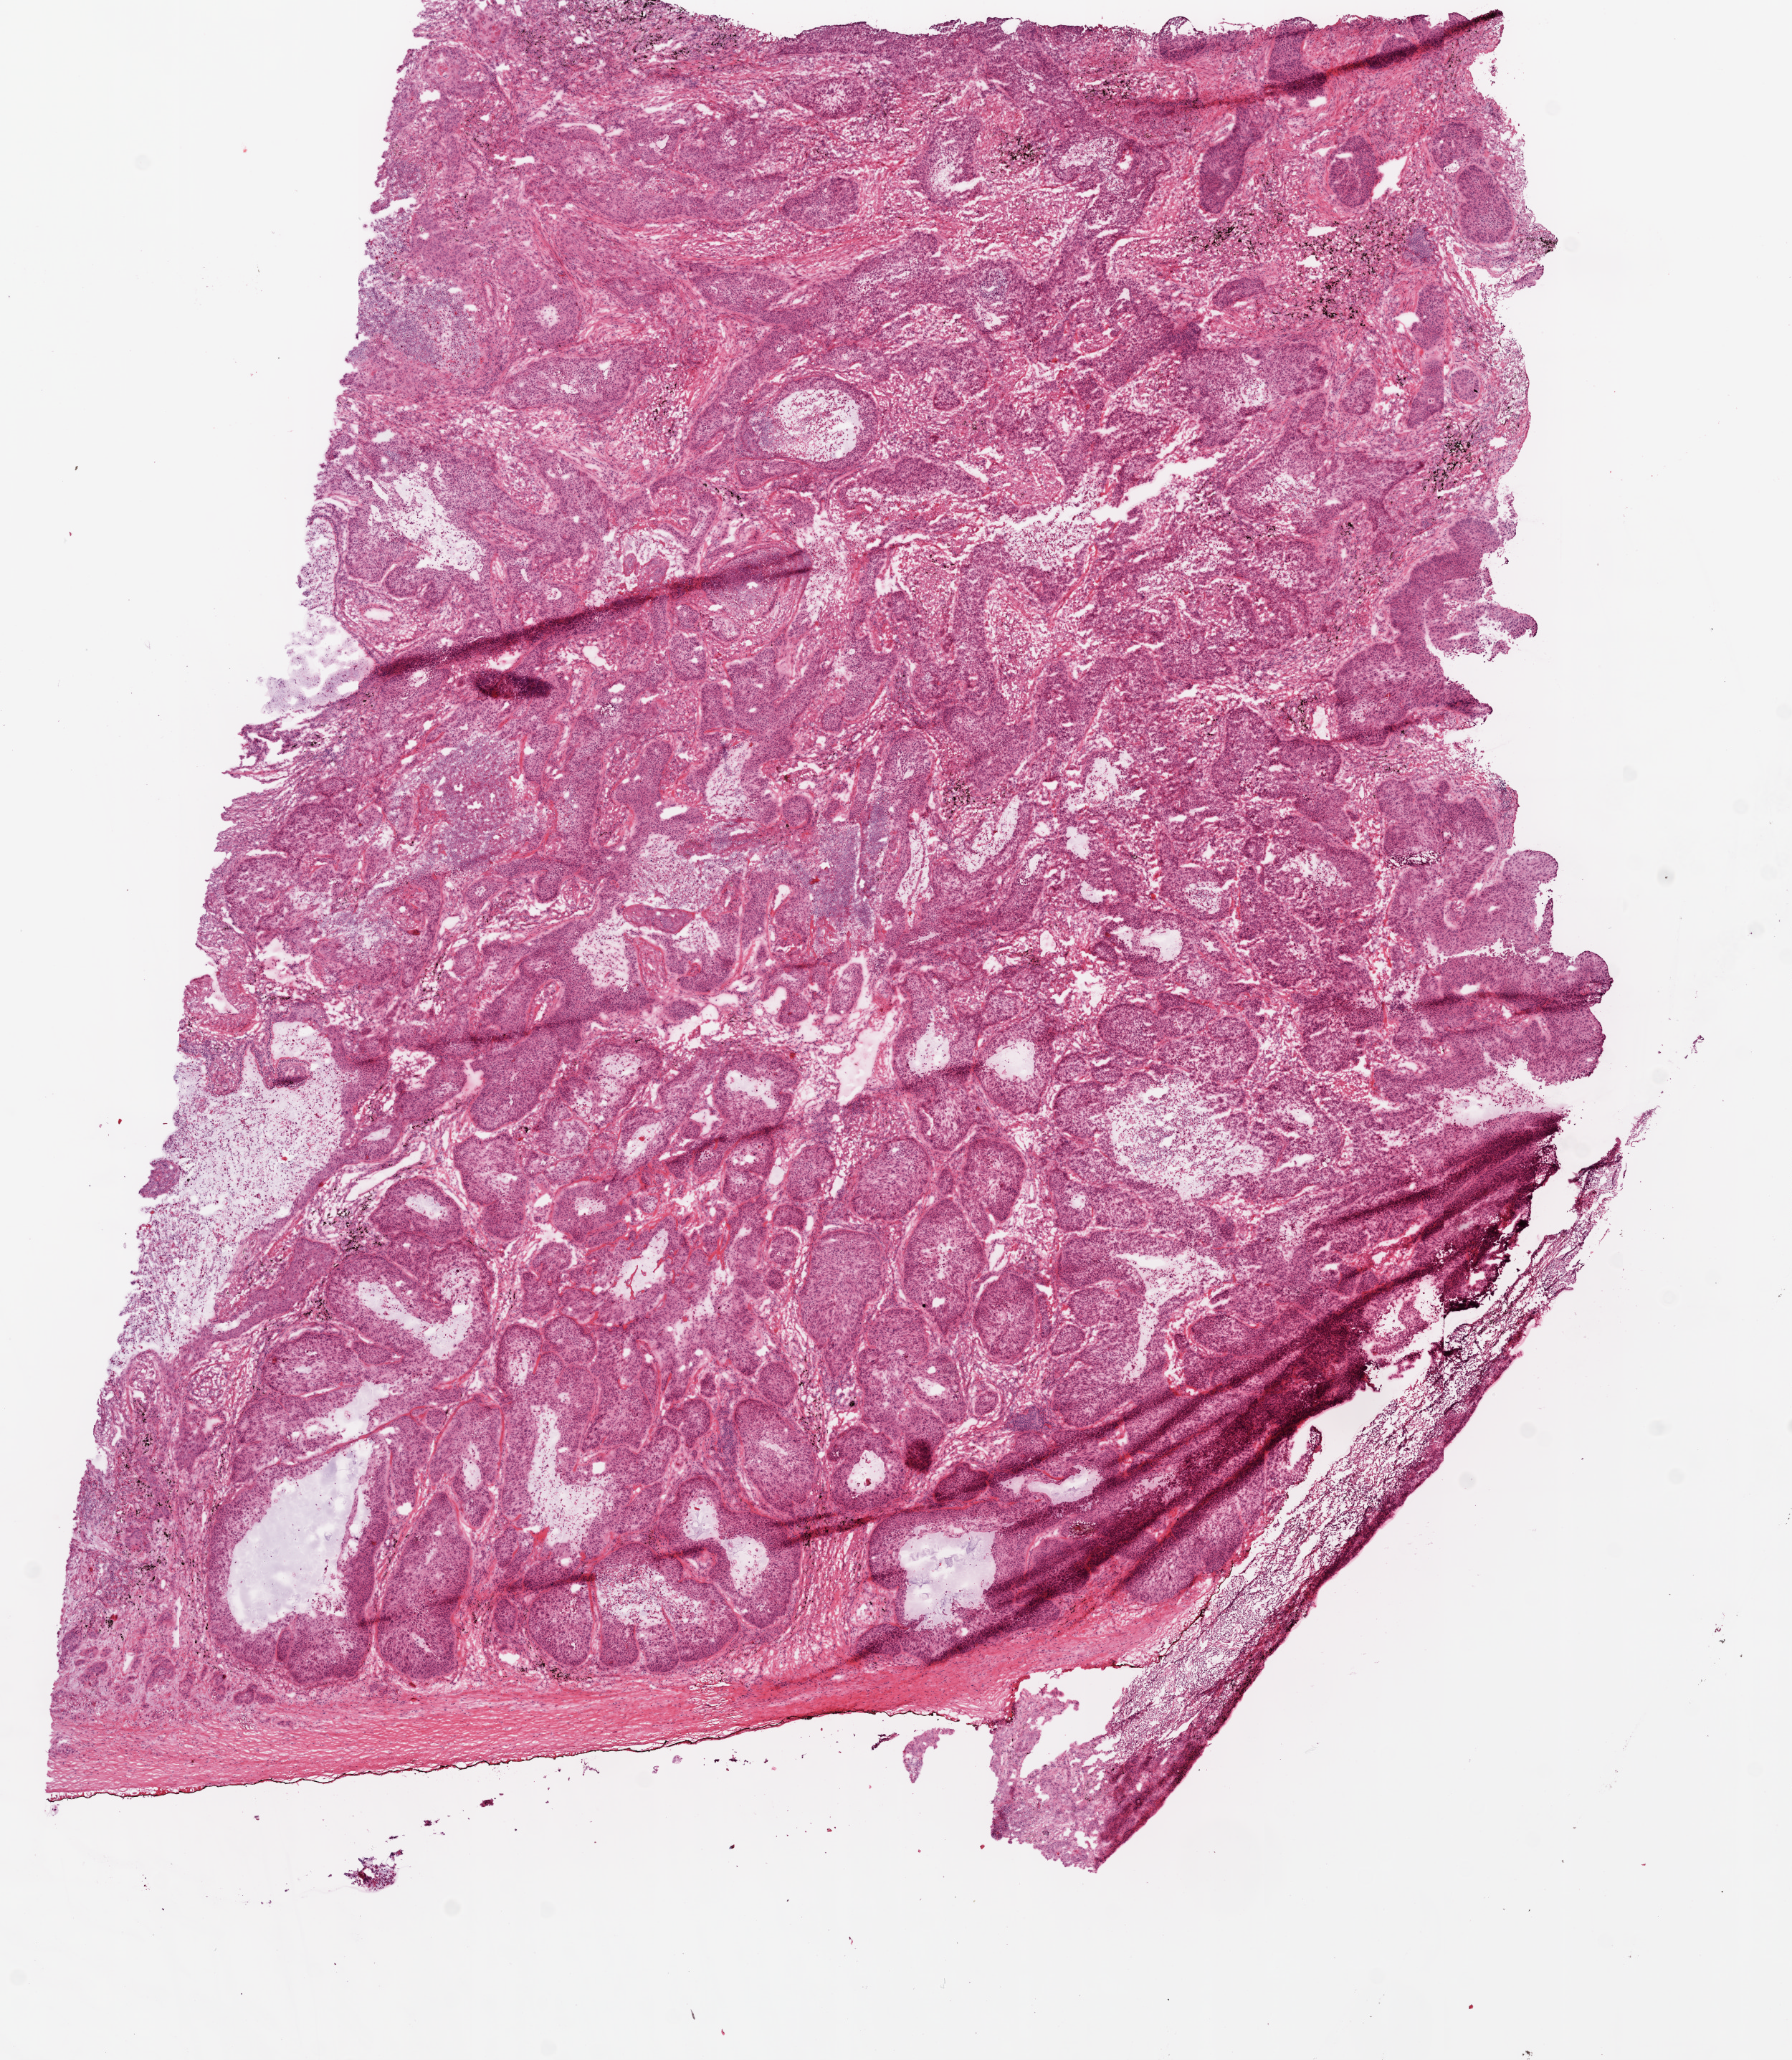
Hematoxylin and eosin (H&E) stained whole-slide image, low-resolution overview of the scanned area, about 10.0 x 11.5 mm. Frozen section from the top of the tissue portion. Sample: primary tumour, lung. Male, age 75 years at initial diagnosis. Slide review estimates, as recorded: tumour cells 60%, tumour nuclei 75%, normal cells 5%, stromal cells 15%, necrosis 20%.
Diagnosis: Squamous cell carcinoma, NOS. TNM: T2a N0 M0. Laterality: right. AJCC pathologic stage: IB.